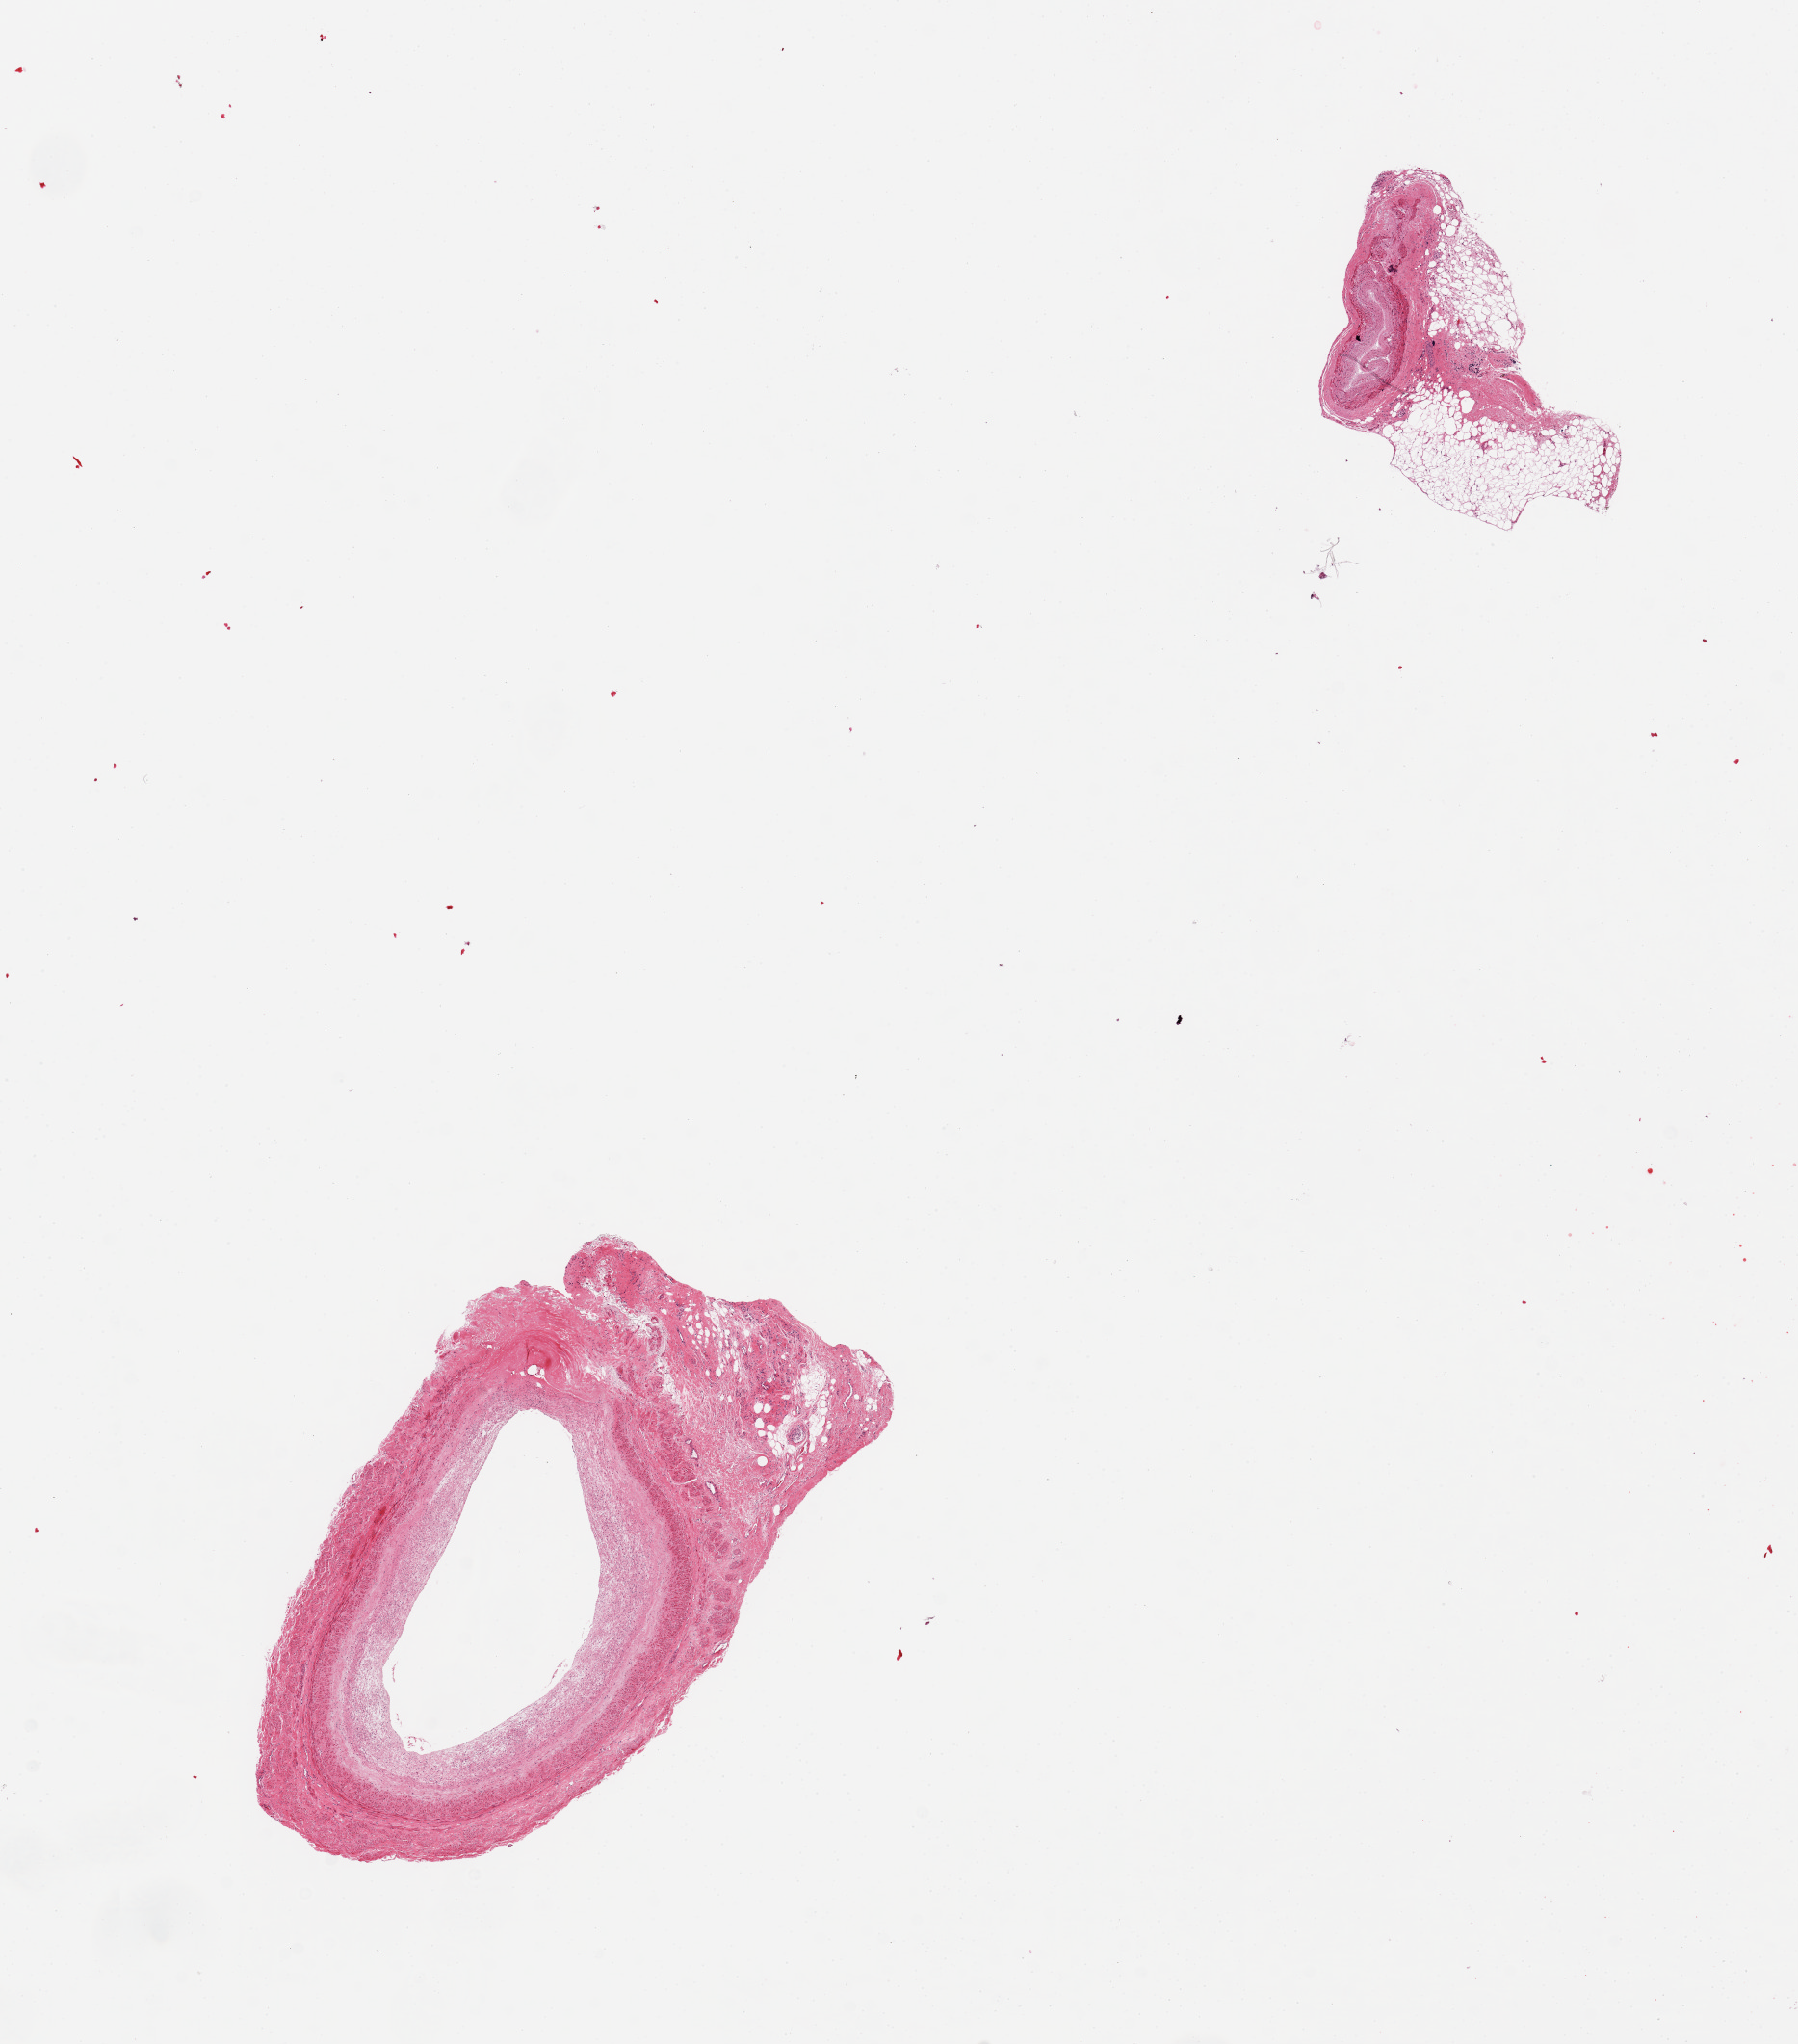
Haematoxylin and eosin whole-slide image, brightfield, low-resolution overview of the scanned area, about 14.8 x 16.8 mm. PAXgene-fixed, paraffin-embedded tissue. Target tissue: coronary artery. Donor tissue sample. Female donor.
Review note (as recorded): 2 pieces, adherent nubbins of fat on both up to ~2mm.